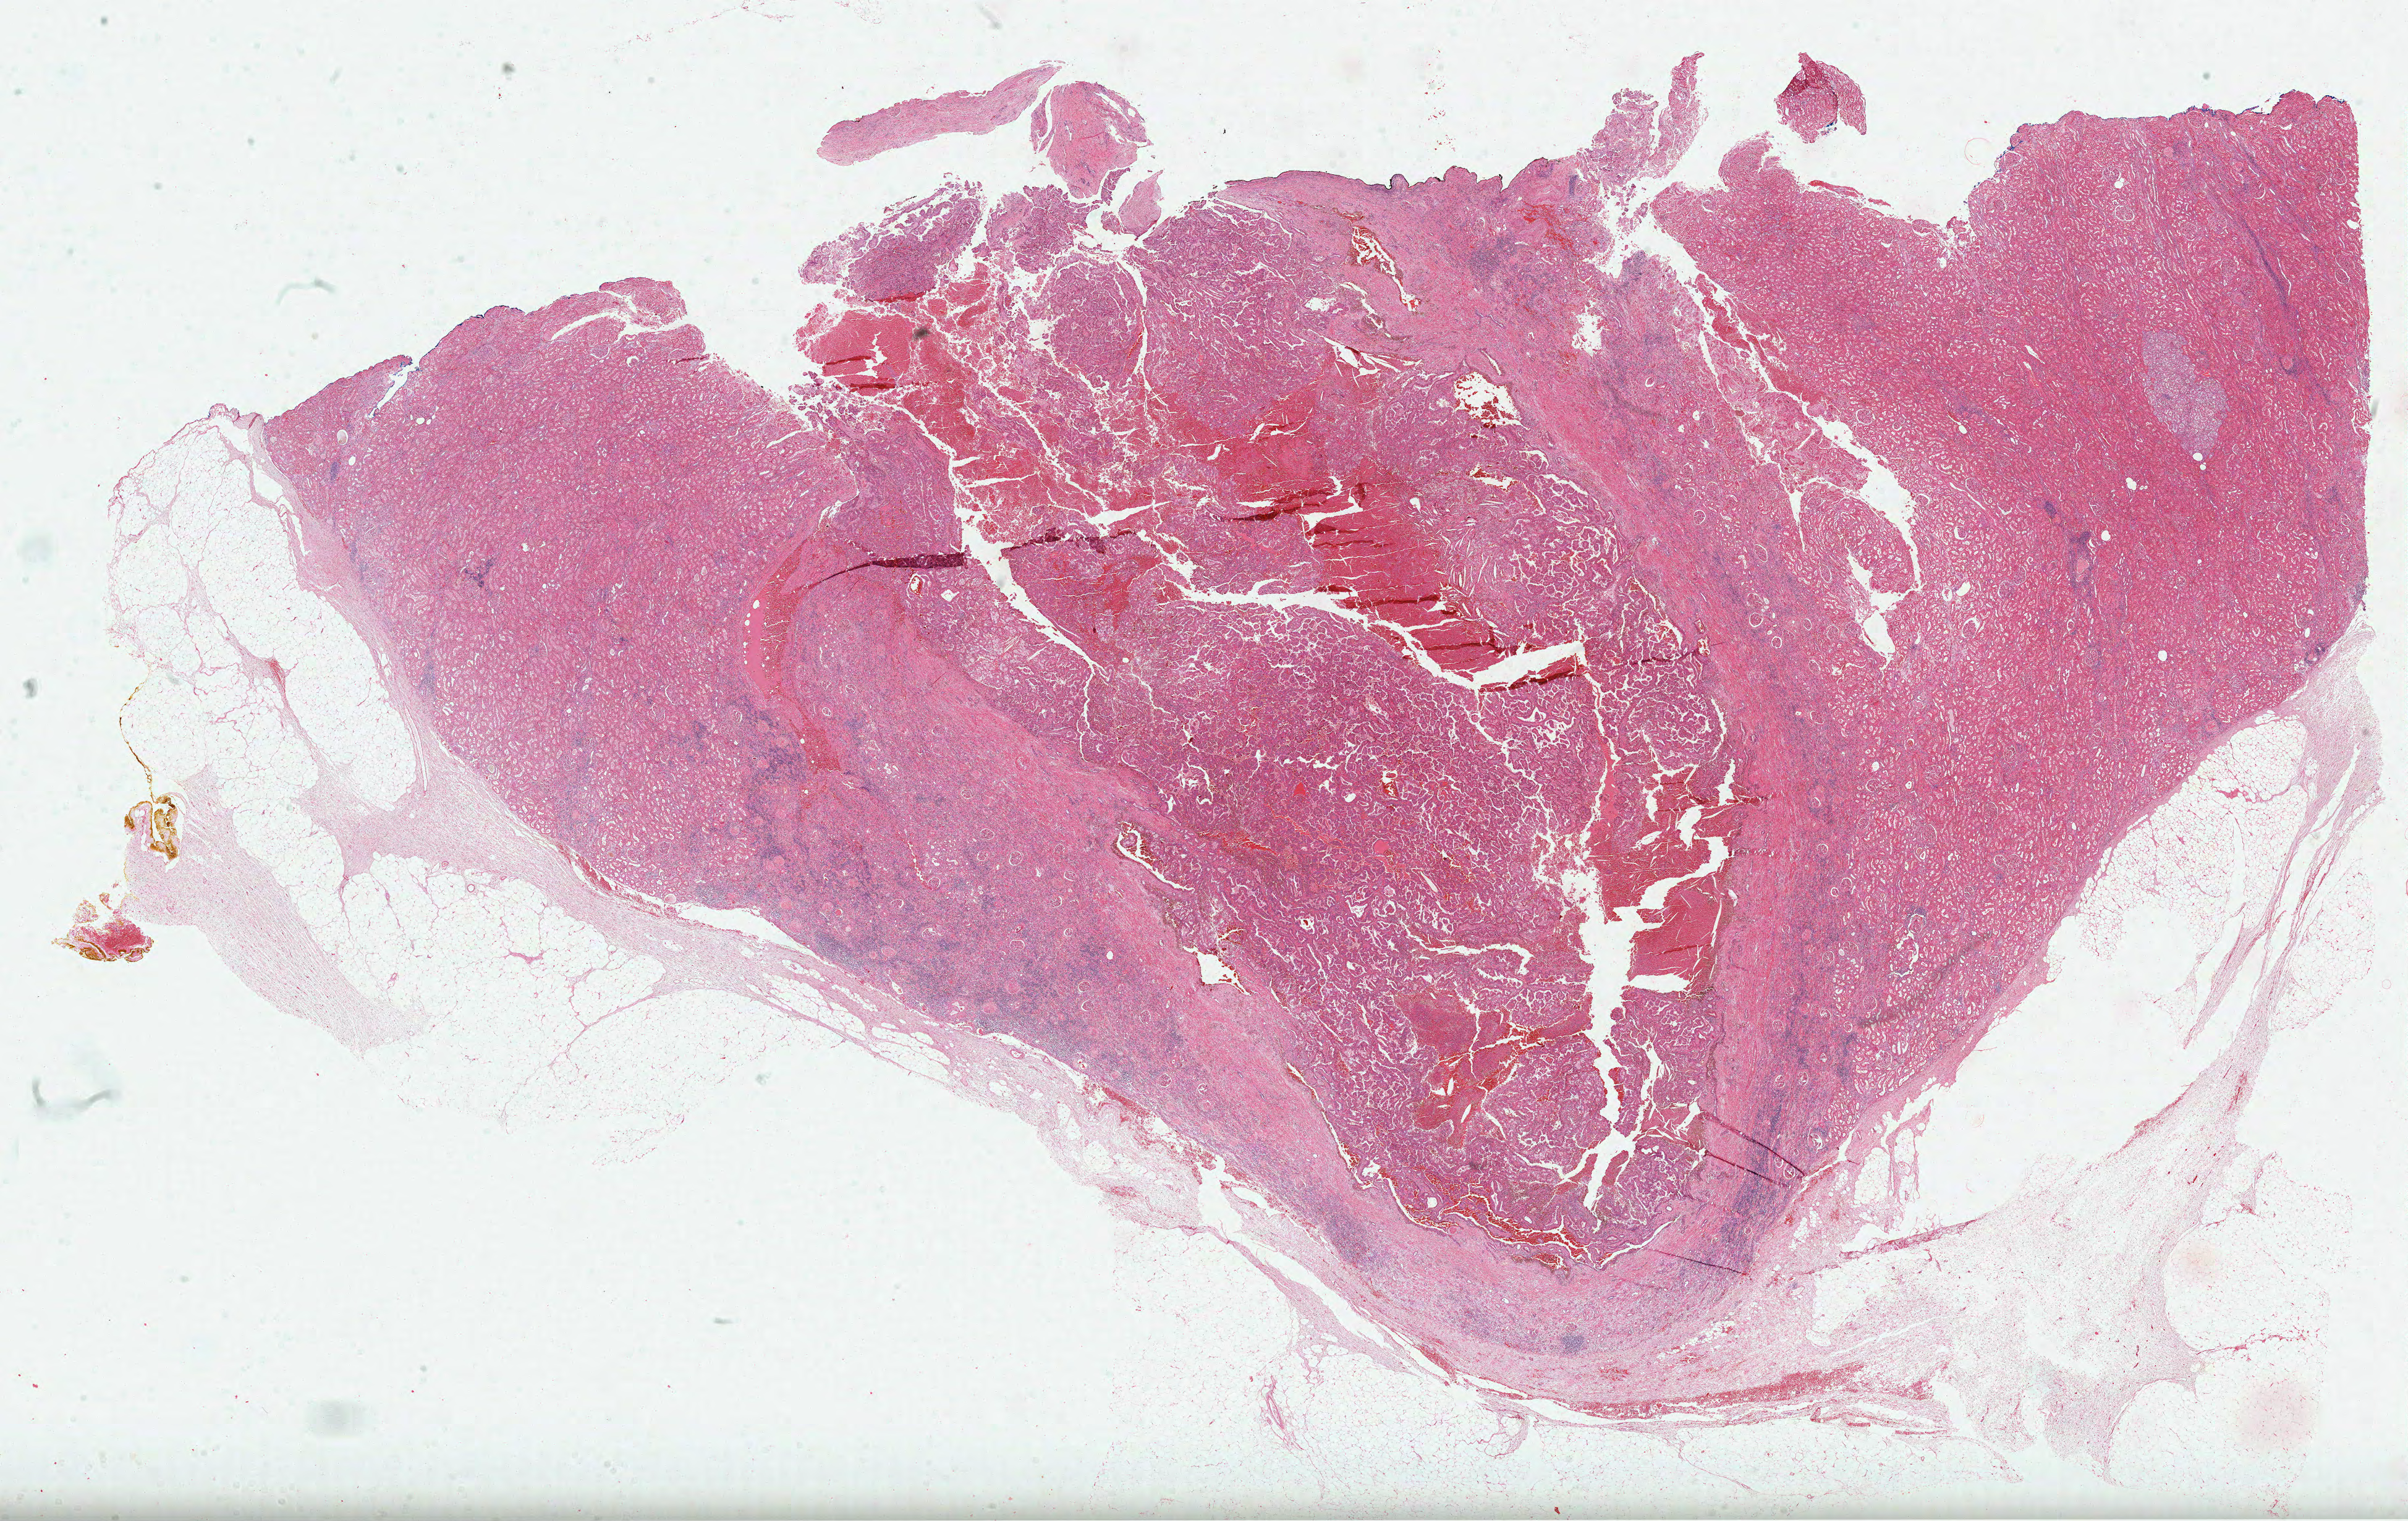
Whole-slide histology image, Hematoxylin and eosin (H&E) stained, shown as a low-resolution overview of the whole scanned area (about 31.4 x 19.9 mm, from a 40x scan). Formalin-fixed paraffin-embedded (FFPE) diagnostic section. Kidney, primary tumour sample. Male patient; age at initial diagnosis 57 years.
AJCC pathologic stage: I (6th edition). TNM: T1a NX MX. Laterality: right. Pathologic diagnosis: Papillary adenocarcinoma, NOS.